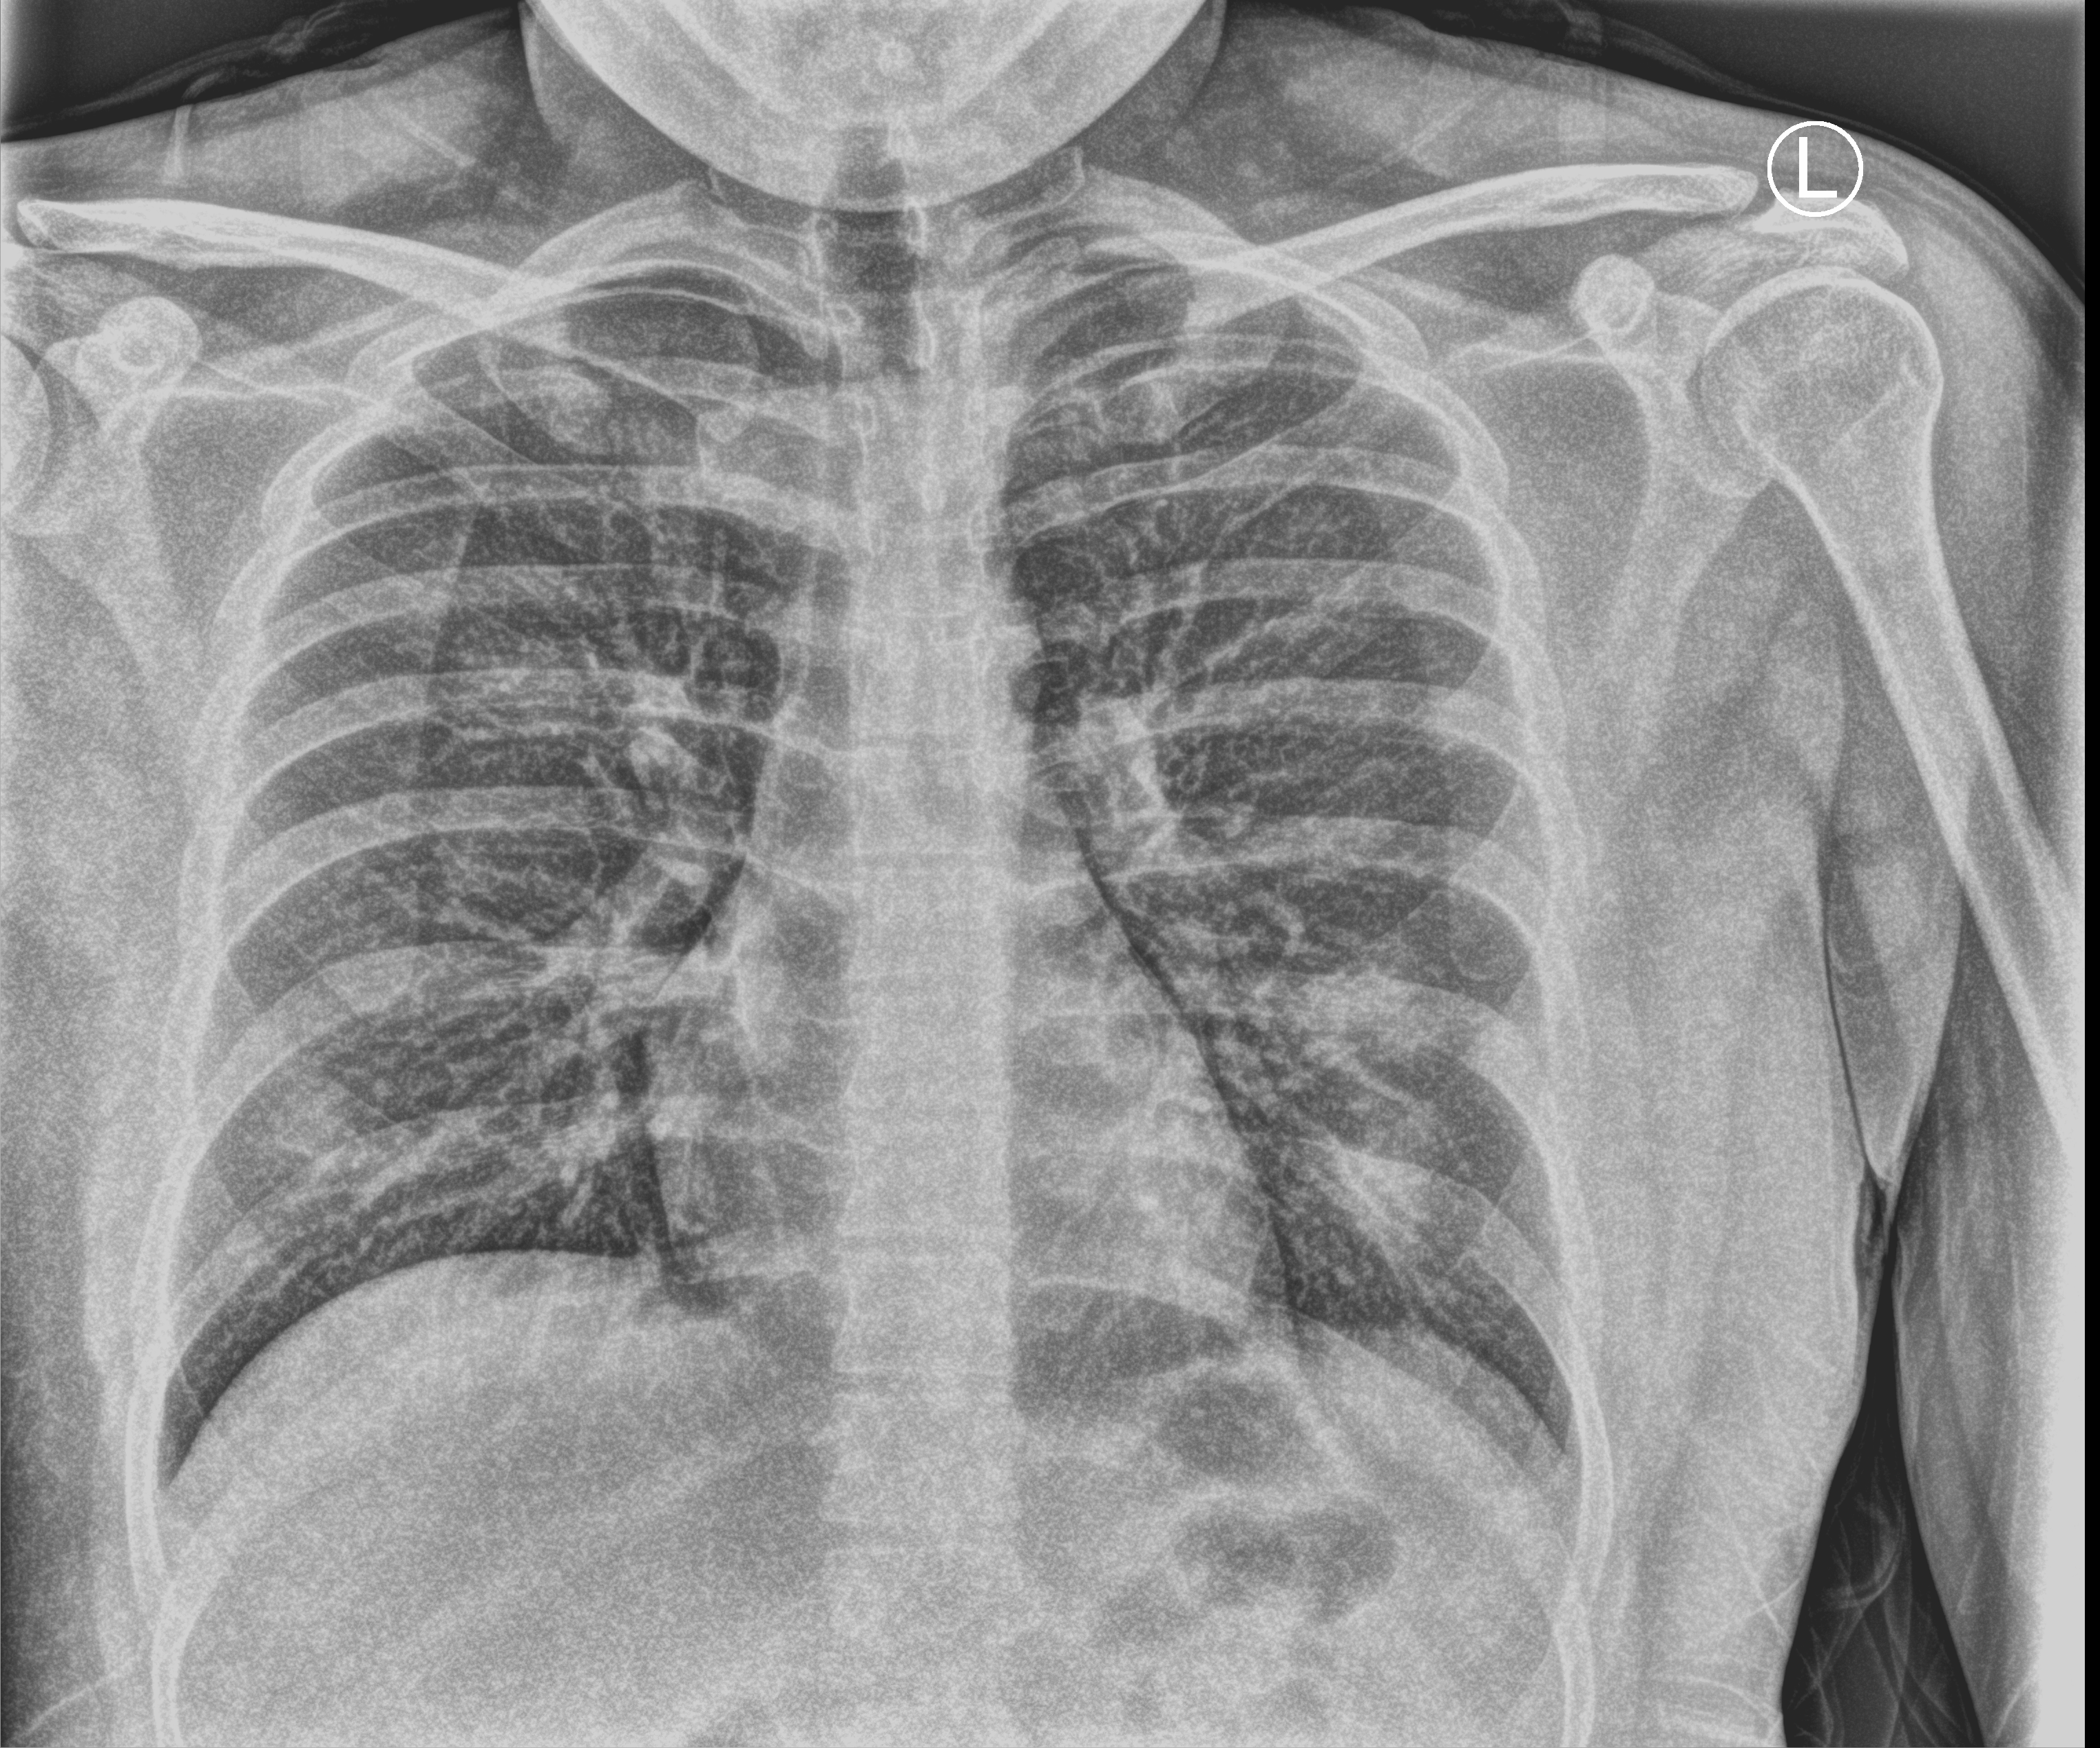
Portable chest radiograph, anteroposterior (AP) projection. Male patient hospitalised with COVID-19, age 18–59 years.
From the hospital-stay record, not from the radiograph (when in the stay this image was taken is not recorded): mechanically ventilated during this hospital stay: no.